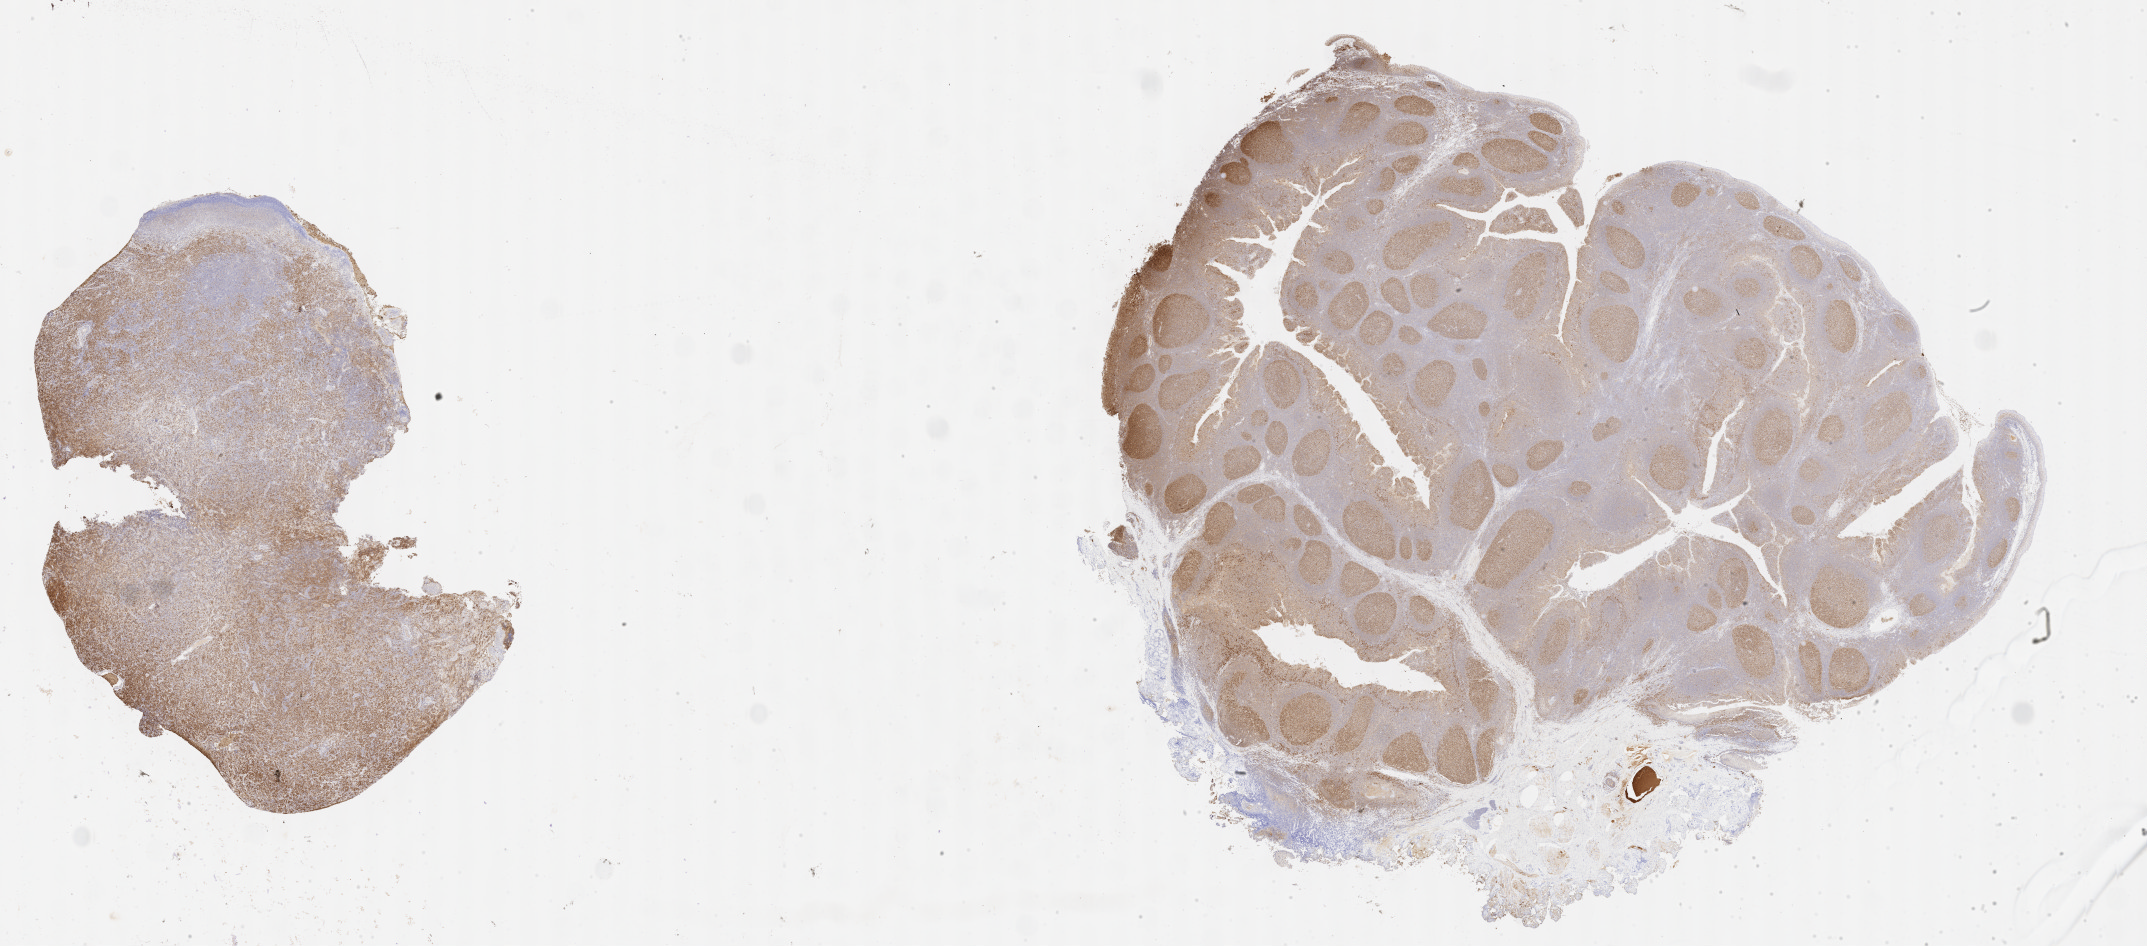
Whole-slide image, immunohistochemical stain for BCL6, shown as a low-resolution overview of the whole scanned area (about 34.7 x 15.3 mm). Tumor tissue. Patient: male, age at initial diagnosis 7 years.
Histologic diagnosis: Diffuse large B-cell lymphoma, NOS.